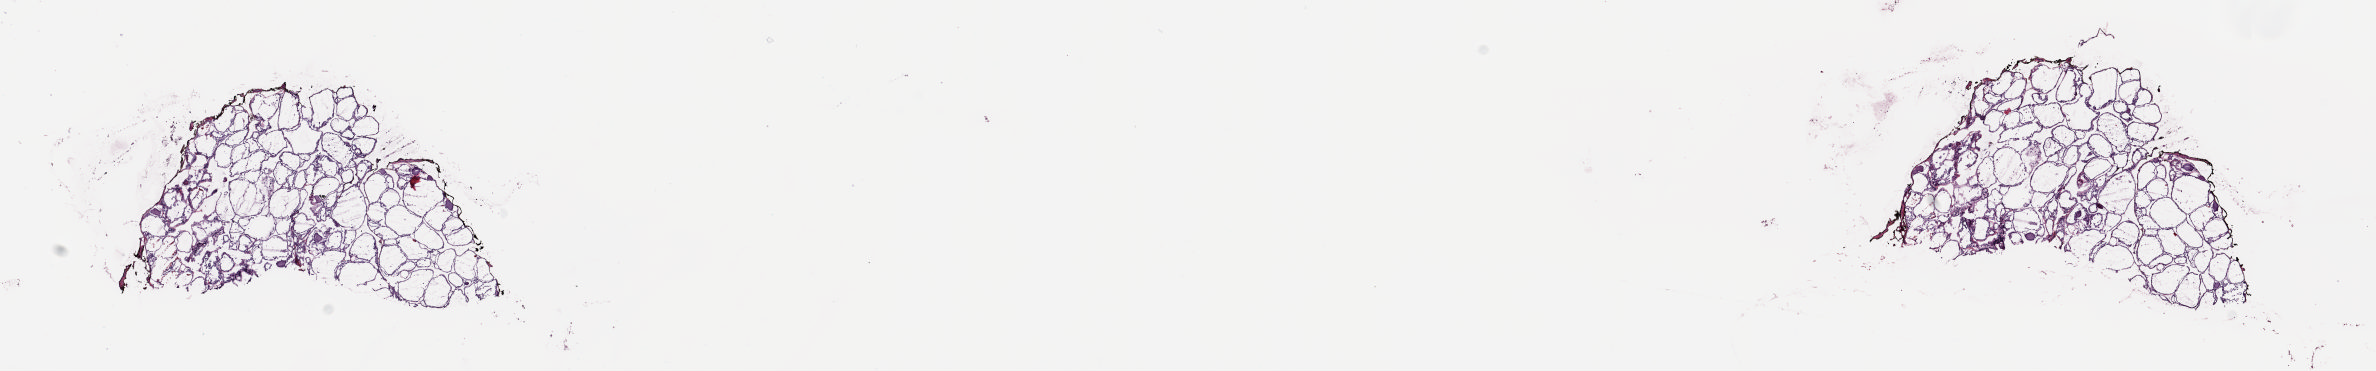
Digitized H&E-stained tissue section (whole slide) — whole scanned area (about 18.8 x 2.9 mm, slide scanned at 20x) shown as a low-resolution overview; frozen section; solid tissue normal (non-tumour tissue) sample from the thyroid. Patient: female, age at initial diagnosis 48 years. Pathologist review of this section (percent, as recorded): tumour cells 0%, tumour nuclei 0%, normal cells 100%, stromal cells 0%, necrosis 0%. Infiltration values recorded for this section: lymphocyte infiltration 1%, monocyte infiltration 4%, neutrophil infiltration 0%.
This section: solid tissue normal sample (biorepository sample class). Patient diagnosis: Papillary carcinoma, follicular variant (thyroid gland).